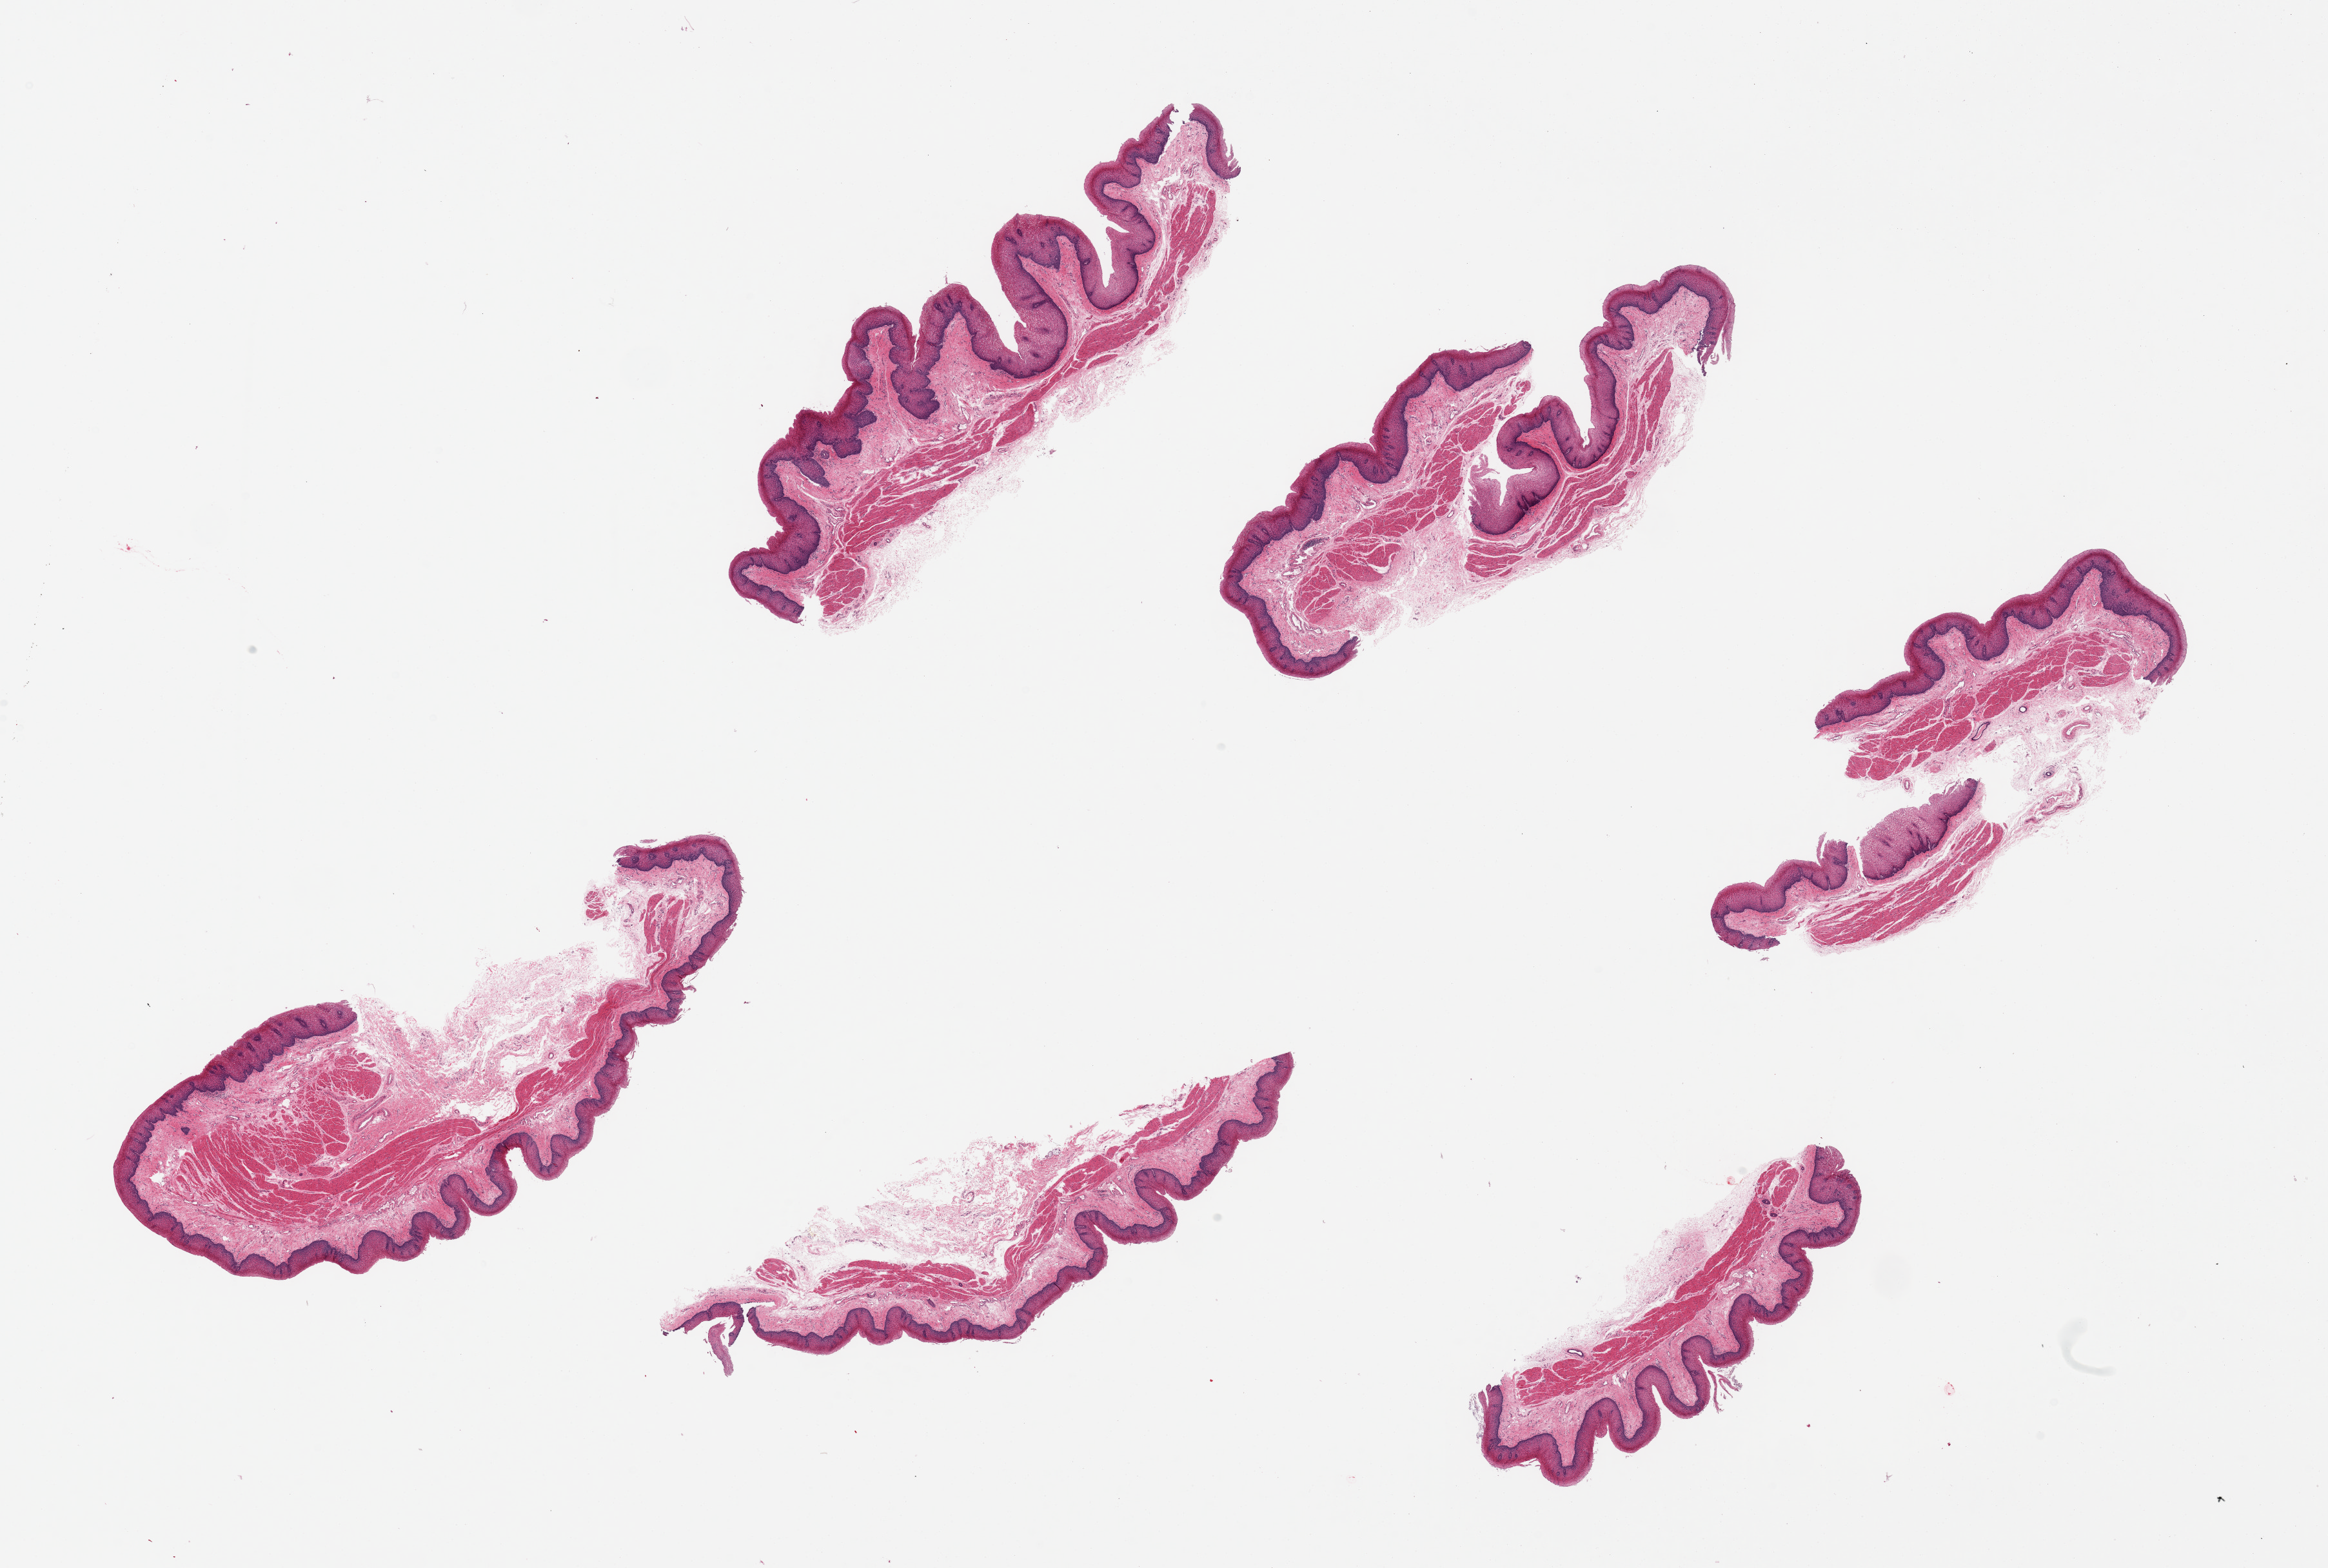
Digitized hematoxylin and eosin (H&E)-stained section — shown as a low-resolution overview of the whole scanned area (about 28.5 x 19.2 mm, acquisition: 20x scan); PAXgene-fixed paraffin-embedded (PFPE) section; target tissue: esophageal mucous membrane; tissue donor sample.
Review note (as recorded): 6 pieces.